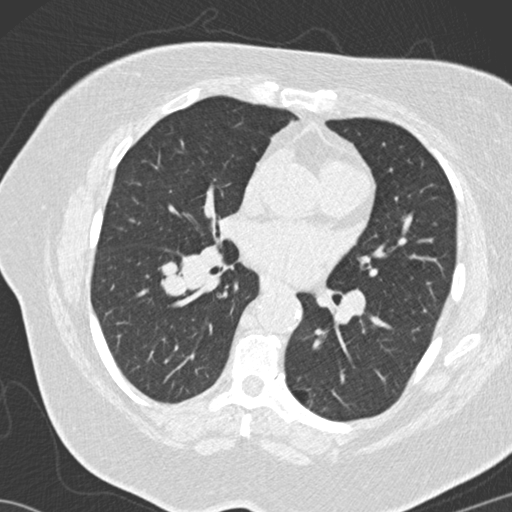
Low-dose screening chest CT, one axial slice; position 70 of 146 along the scan axis; 120 kVp; lung window (W 1500 / L -600 HU); 2 mm slice thickness; 512 × 512 image matrix, field of view 350 × 350 mm.
Outlined on this slice (outlined manually by an expert reader):
- lesion 4 (tumor, lower lobe of right lung): box from (x=160, y=262) to (x=187, y=298) px